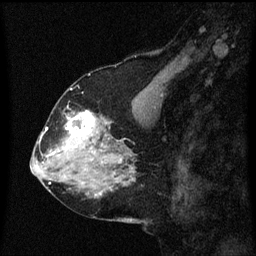
Breast MRI (dynamic contrast-enhanced), one sagittal slice; slice 27 of 60 in the series (ordered by position); dynamic contrast-enhanced series, image 2 of 3 at this slice position (ordered by acquisition); 1.5 T; TE 4.2 ms, TR 8.4 ms; 2 mm slice thickness; 256 × 256 image matrix, field of view 200 × 200 mm. Patient: female, 58 years.
Structures marked on this image (semi-automatically segmented with operator editing):
- analysis volume of interest (the breast-tissue region the enhancement analysis was run in; not a lesion): bounding box (x1, y1, x2, y2) in pixels: (58, 108, 99, 151)
- tumour enhancement mask (voxels above the 70 % enhancement threshold inside the analysis volume of interest): (62, 112, 97, 151)